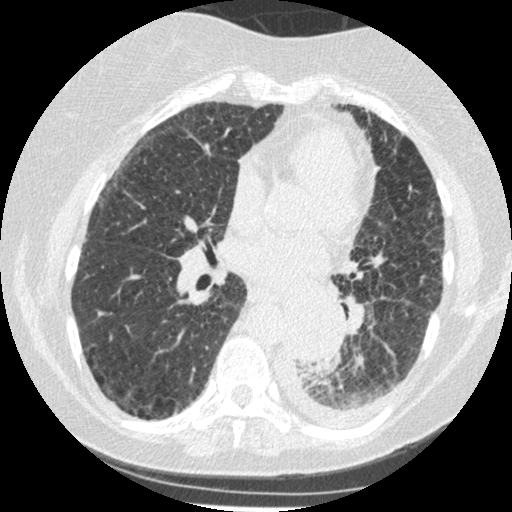
Low-dose screening chest CT, one axial slice; position 113 of 341 along the scan axis; lung window (W 1500 / L -600 HU); 1.25 mm slice thickness; 512 × 512 image matrix, field of view 310 × 310 mm.
Structures marked on this image (manually delineated by an expert):
- lesion 1 (tumor, lower lobe of left lung): bounding box (x1, y1, x2, y2) in pixels: (284, 302, 340, 364)